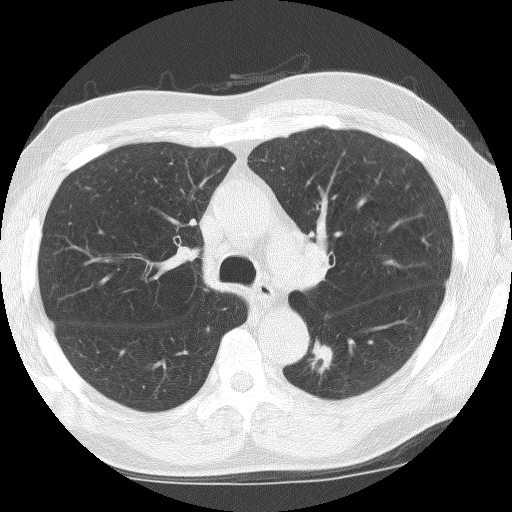
Low-dose screening chest CT, one axial slice. Position 99 of 155 along the scan axis. 120 kVp. Lung window (W 1500 / L -600 HU). 2.5 mm slice thickness. 512 × 512 image matrix, field of view 323 × 323 mm.
Annotated regions visible in this slice (outlined manually by an expert reader):
- lesion 1 (tumor, lower lobe of left lung): bounding box <310,339,333,375> (left, top, right, bottom; pixels)